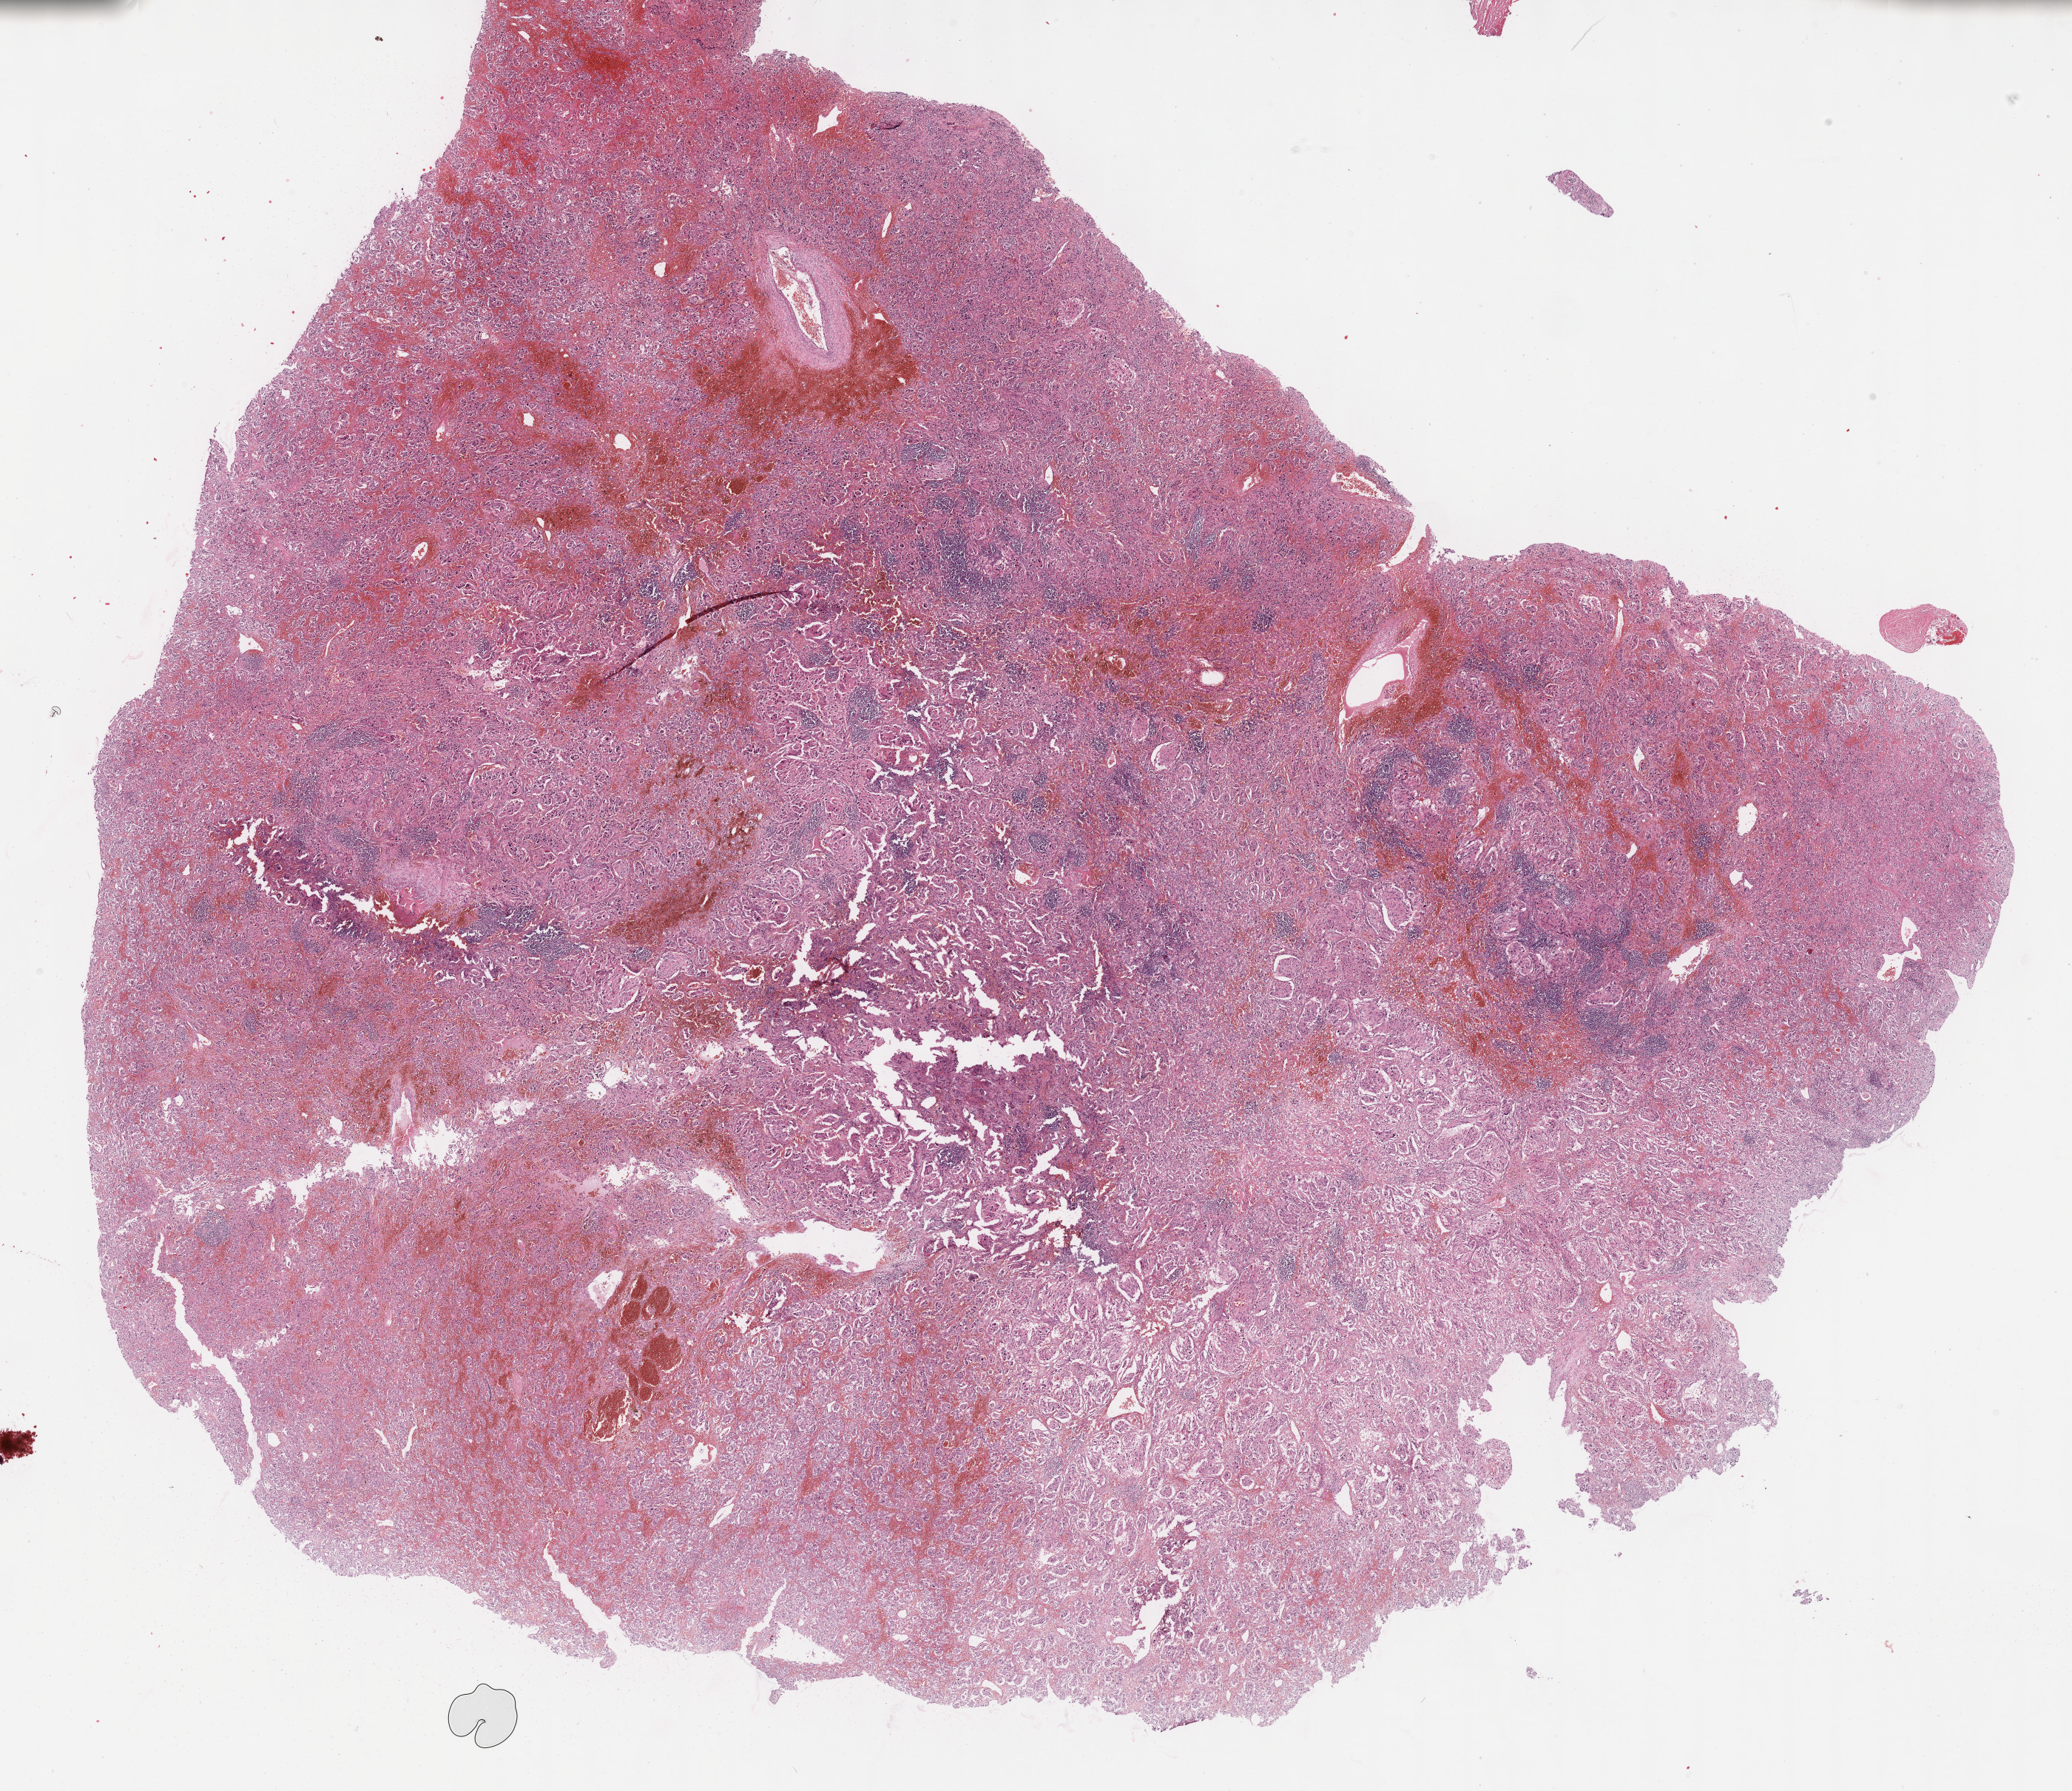
Digitized H&E tissue section (whole slide) — shown as a low-resolution overview of the whole scanned area (about 22.7 x 19.6 mm, slide scanned at 40x), formalin-fixed paraffin-embedded (FFPE) diagnostic section, primary tumour sample from the adrenal gland. Male patient; age at initial diagnosis 19 years.
* laterality: right
* pathologic diagnosis: Pheochromocytoma, malignant